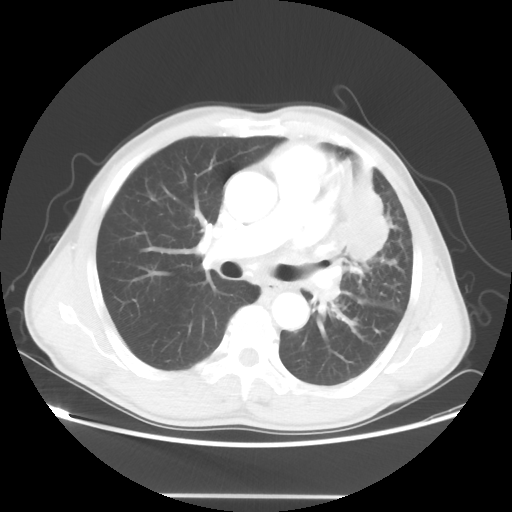
Chest CT, one axial slice; position 30 of 55 along the scan axis; reconstruction kernel STANDARD; 100 kVp; lung window (W 1500 / L -600 HU); 5 mm slice thickness; 512 × 512 image matrix. Male patient, age 60 years. From the clinical record (not read from this slice): clinical TNM (as recorded): T3 N3 M0.
Outlined on this slice (bounding box drawn by a radiologist):
- lung tumour (recorded histology: adenocarcinoma): box from (x=348, y=165) to (x=395, y=268) px